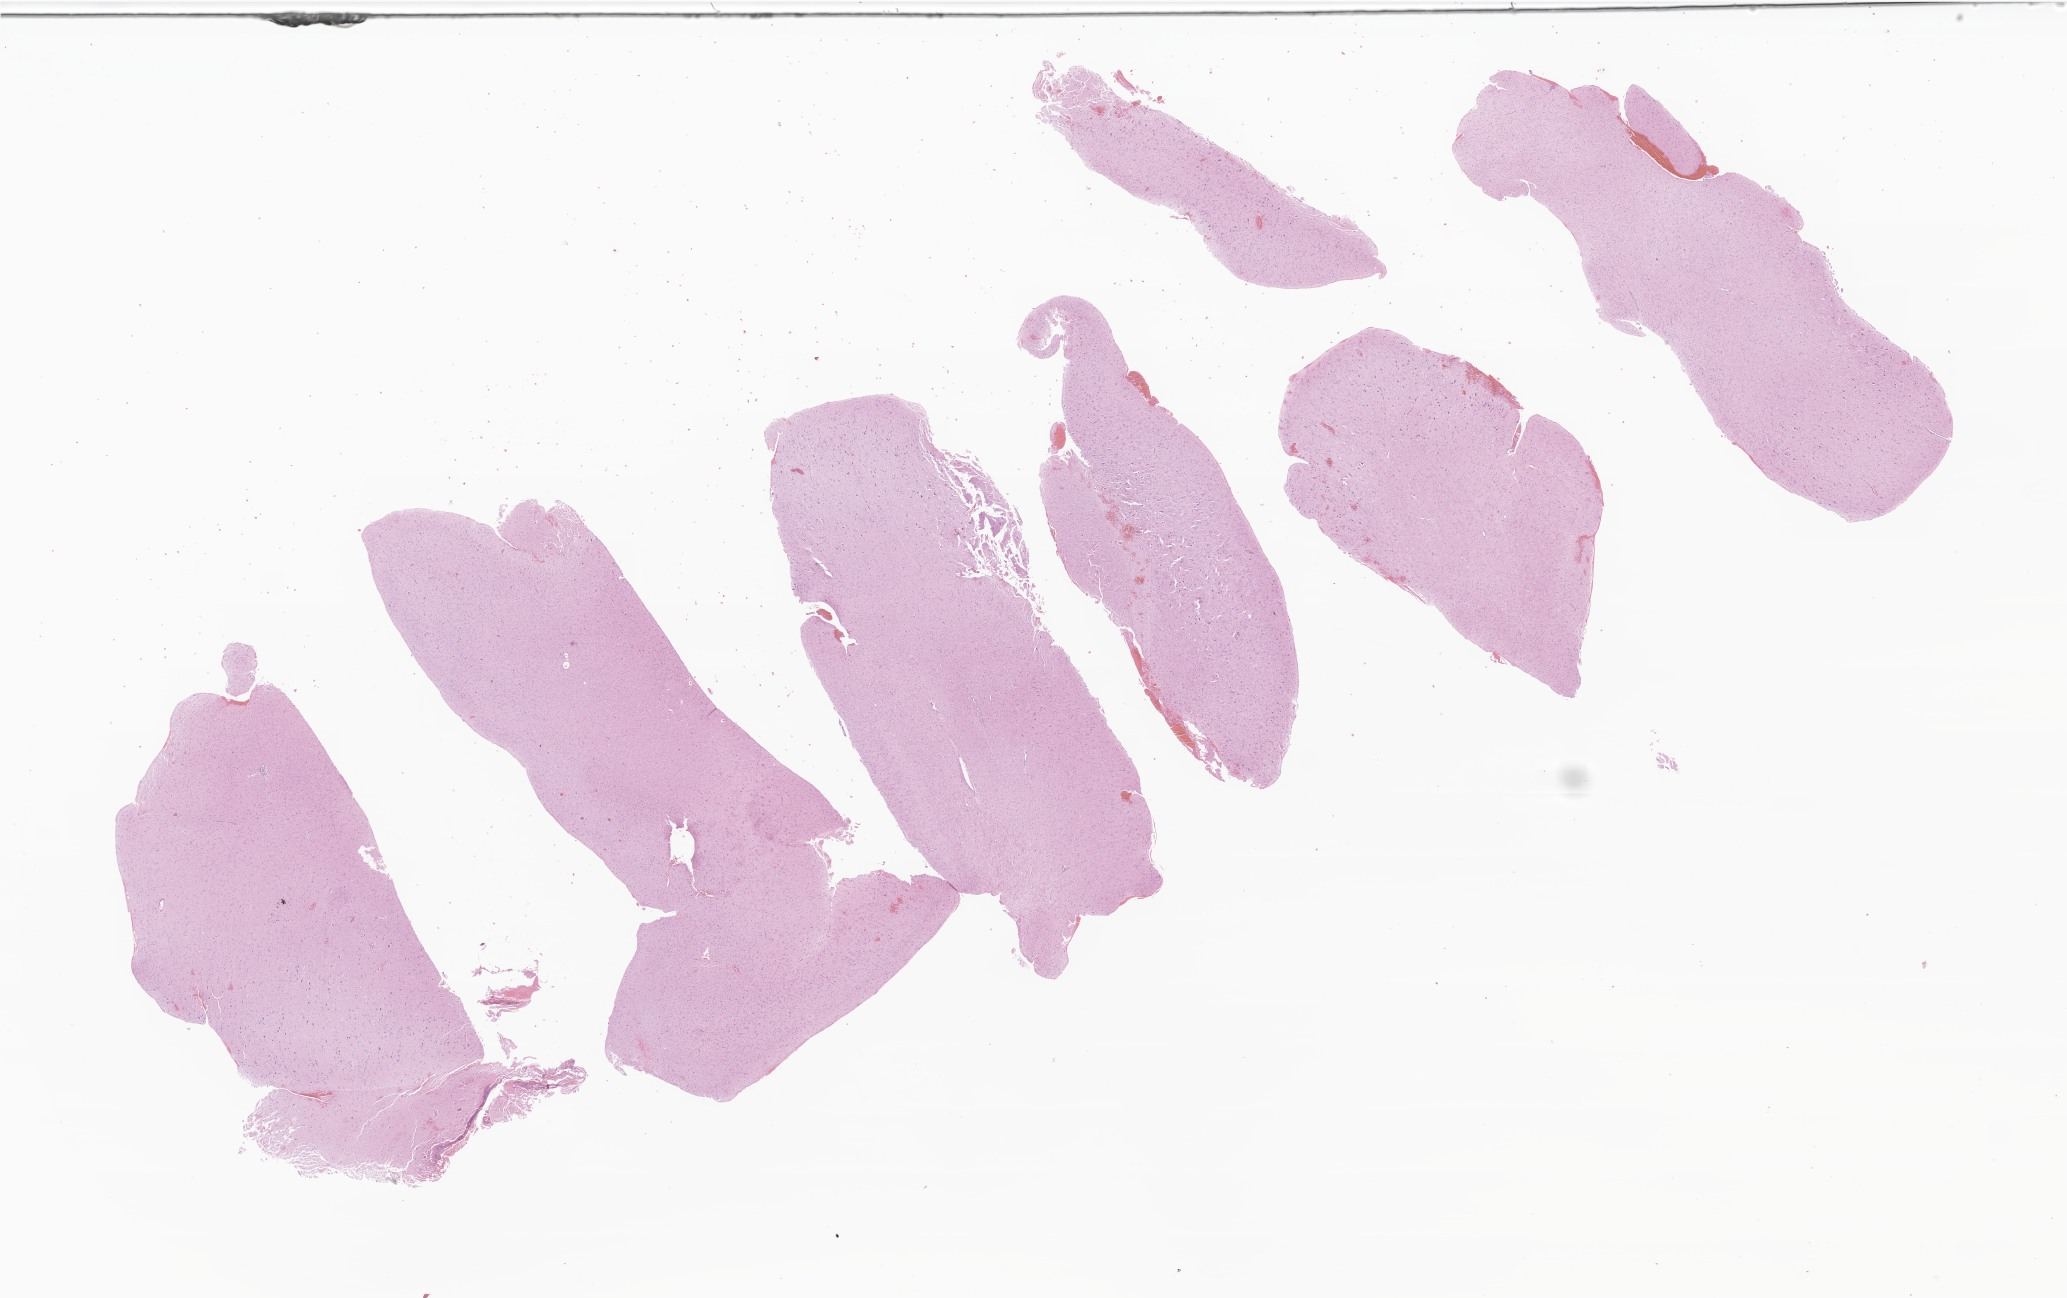
Whole-slide image, haematoxylin and eosin stain of tumor tissue from the parietal lobe, a low-resolution overview of the entire scanned area, about 34.9 x 21.9 mm. Formalin-fixed paraffin-embedded section. Female patient, age 113 months (9 years 5 months).
Recorded diagnosis: Ganglioglioma, NOS.